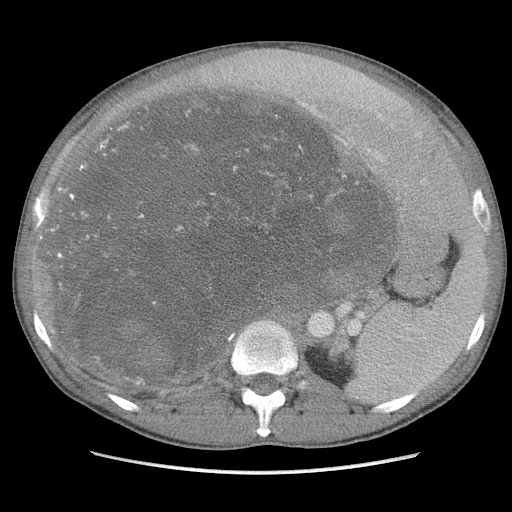
Contrast-enhanced abdominal CT, one axial slice. Position 68 of 115 along the scan axis. Soft-tissue window (W 400 / L 40 HU). 5 mm slice thickness. 512 × 512 image matrix, field of view 360 × 360 mm. Male patient. Case-level facts recorded for this patient, not image findings: diagnosis: adrenocortical carcinoma; tumour side: right adrenal; Ki-67 index: 13 %; stage (as recorded): 3.
Structures marked on this image (semi-automatically segmented with operator editing):
- mass: bounding box [x1, y1, x2, y2] px = [52, 91, 382, 381]